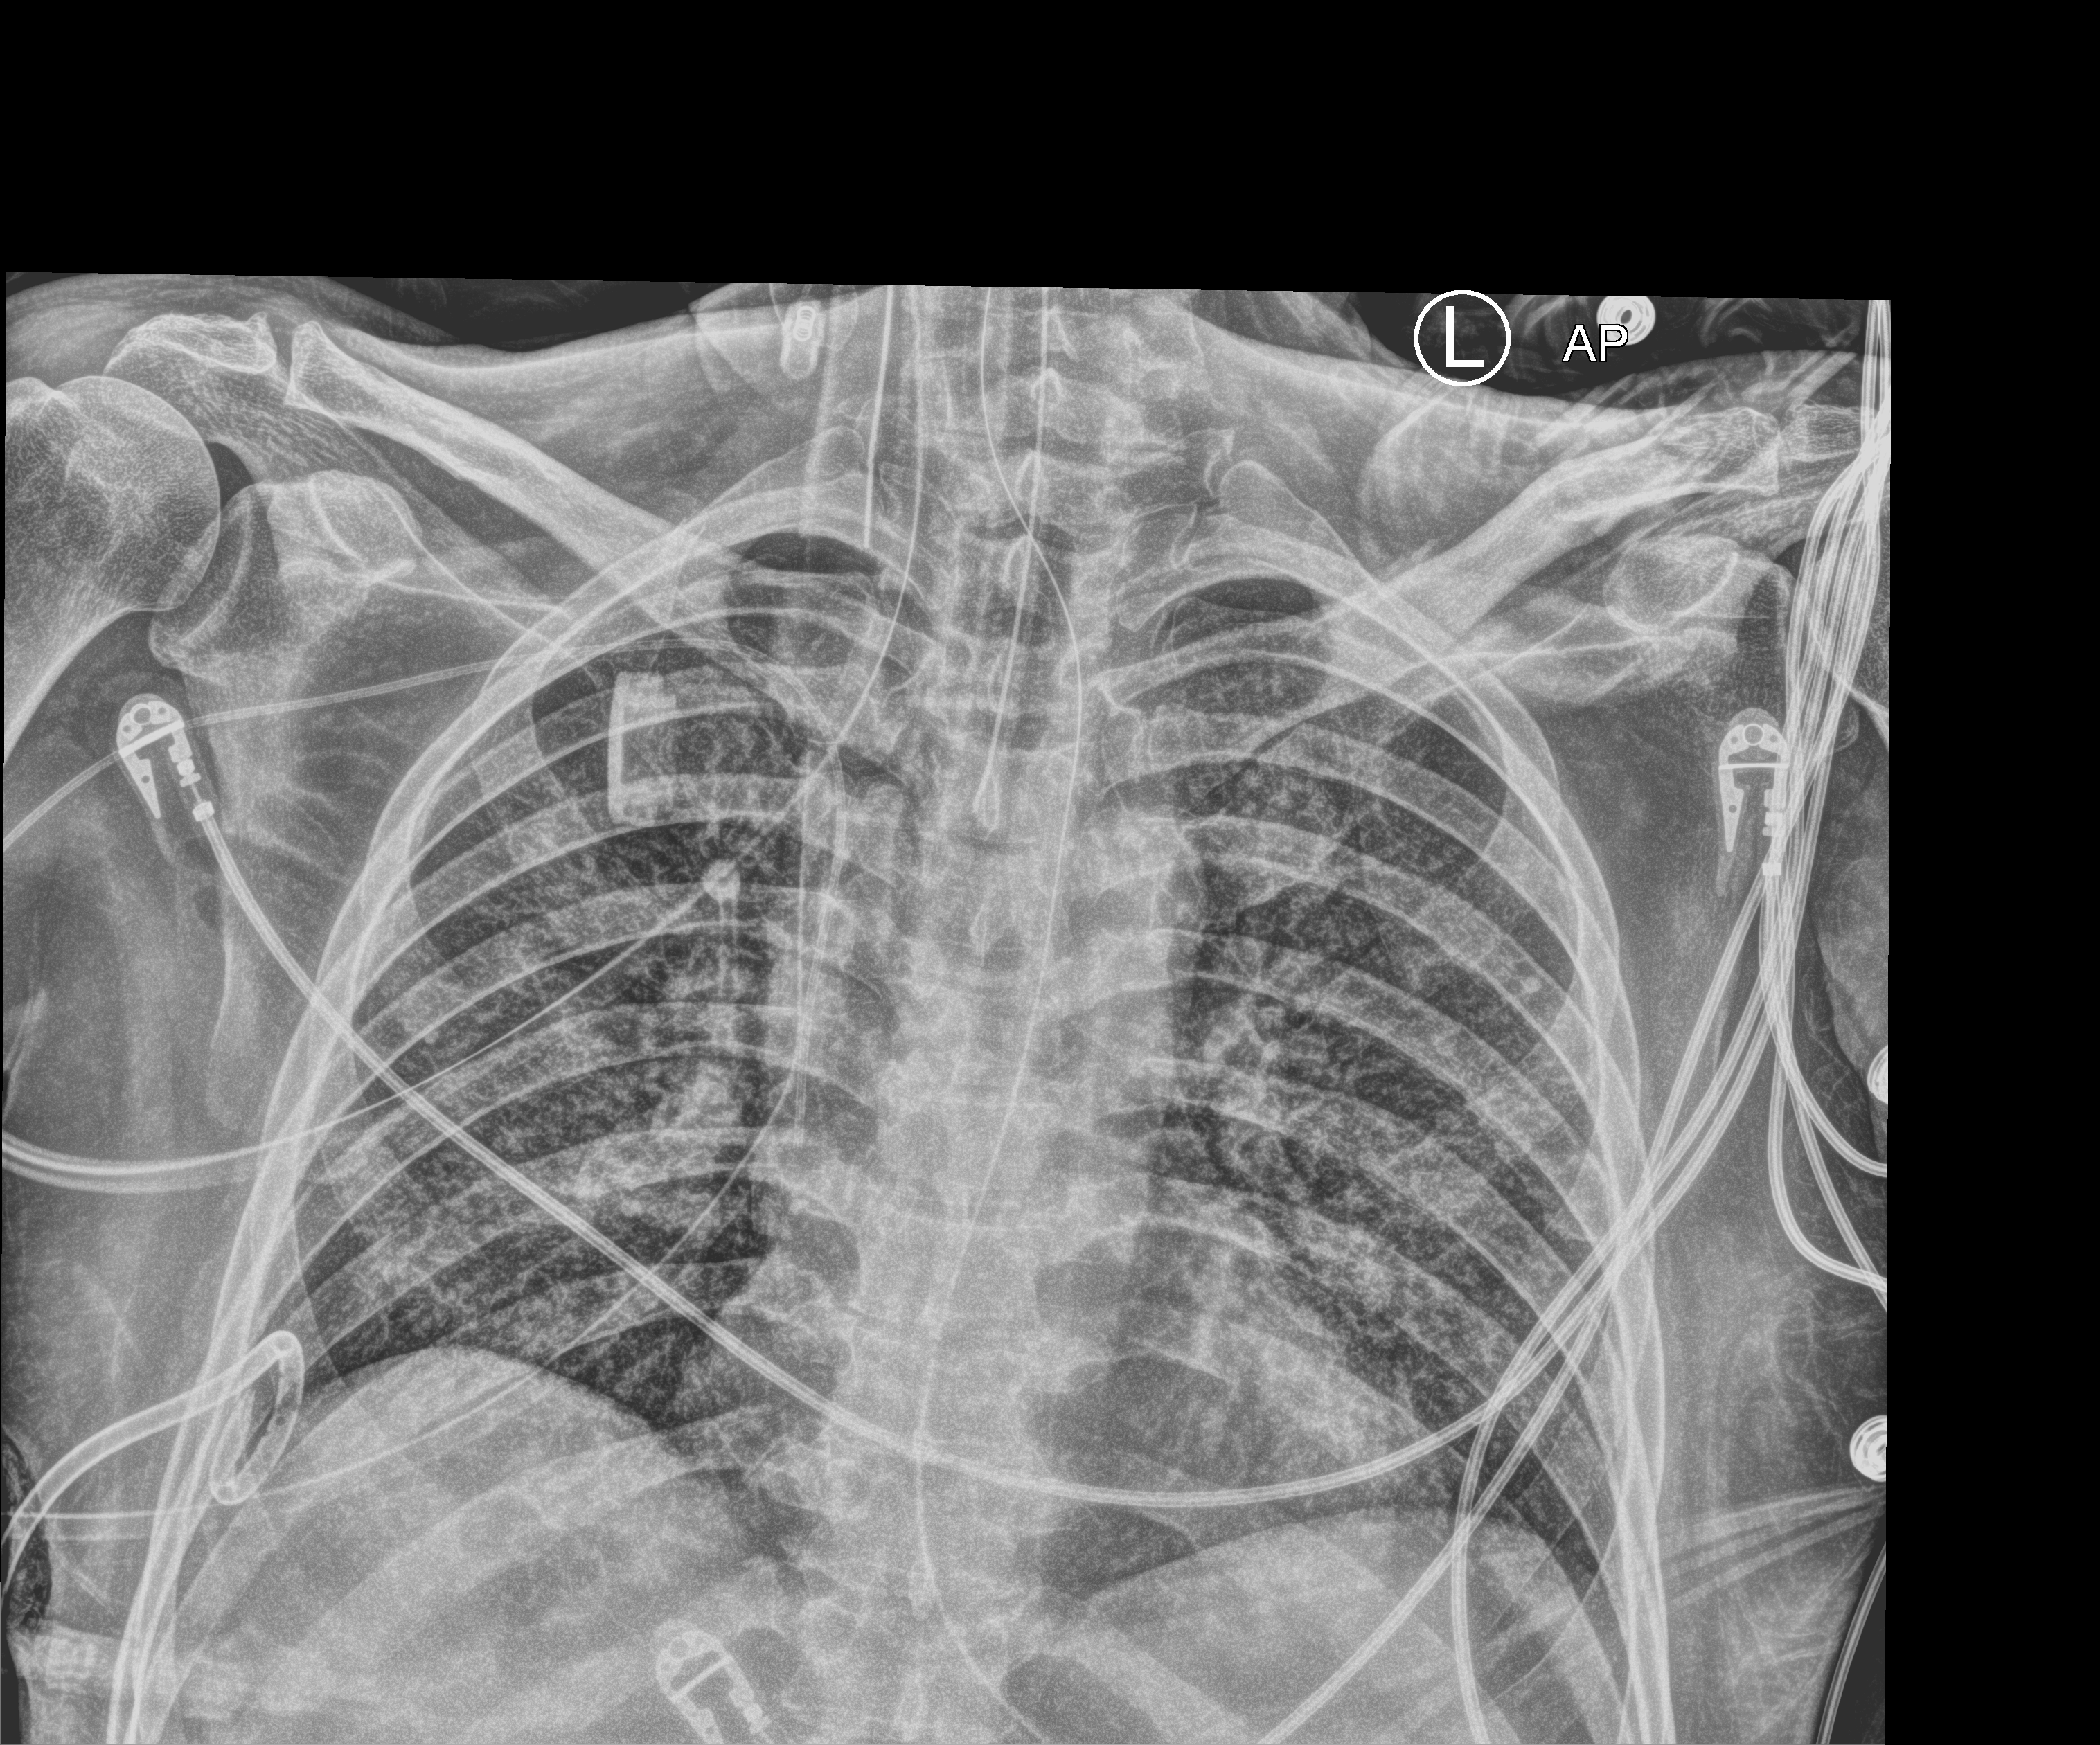
Portable chest radiograph; anteroposterior (AP) projection. Patient hospitalised with COVID-19; male, aged 18–59 years.
Hospital-stay facts (about this admission, not read from this image; timing relative to this image not recorded): mechanically ventilated during this hospital stay: yes.